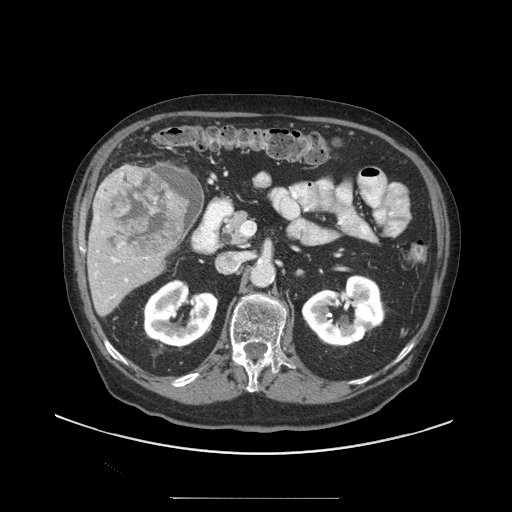
Contrast-enhanced abdominal CT (liver protocol), one axial slice; slice 46 of 97 in the series (ordered by position); reconstruction kernel STANDARD; 140 kVp; soft-tissue window (W 400 / L 40 HU); 2.5 mm slice thickness; 512 × 512 image matrix. Case-level facts recorded for this patient, not image findings: diagnosis: hepatocellular carcinoma (patient treated with transarterial chemoembolisation; whether this scan precedes or follows treatment is not stated here); TNM stage (as recorded): Stage-IIIC; Child-Pugh class: A; tumour differentiation: well differentiated; tumour nodularity: uninodular.
Annotated regions visible in this slice (semi-automatically segmented with operator editing):
- liver parenchyma outside the tumour (the mass and vessels are separate outlines, so this box may not span the whole liver): box from (x=88, y=164) to (x=200, y=316) px
- mass: (x=96, y=166)–(x=187, y=258)
- liver vessels: (x=95, y=251)–(x=127, y=298)